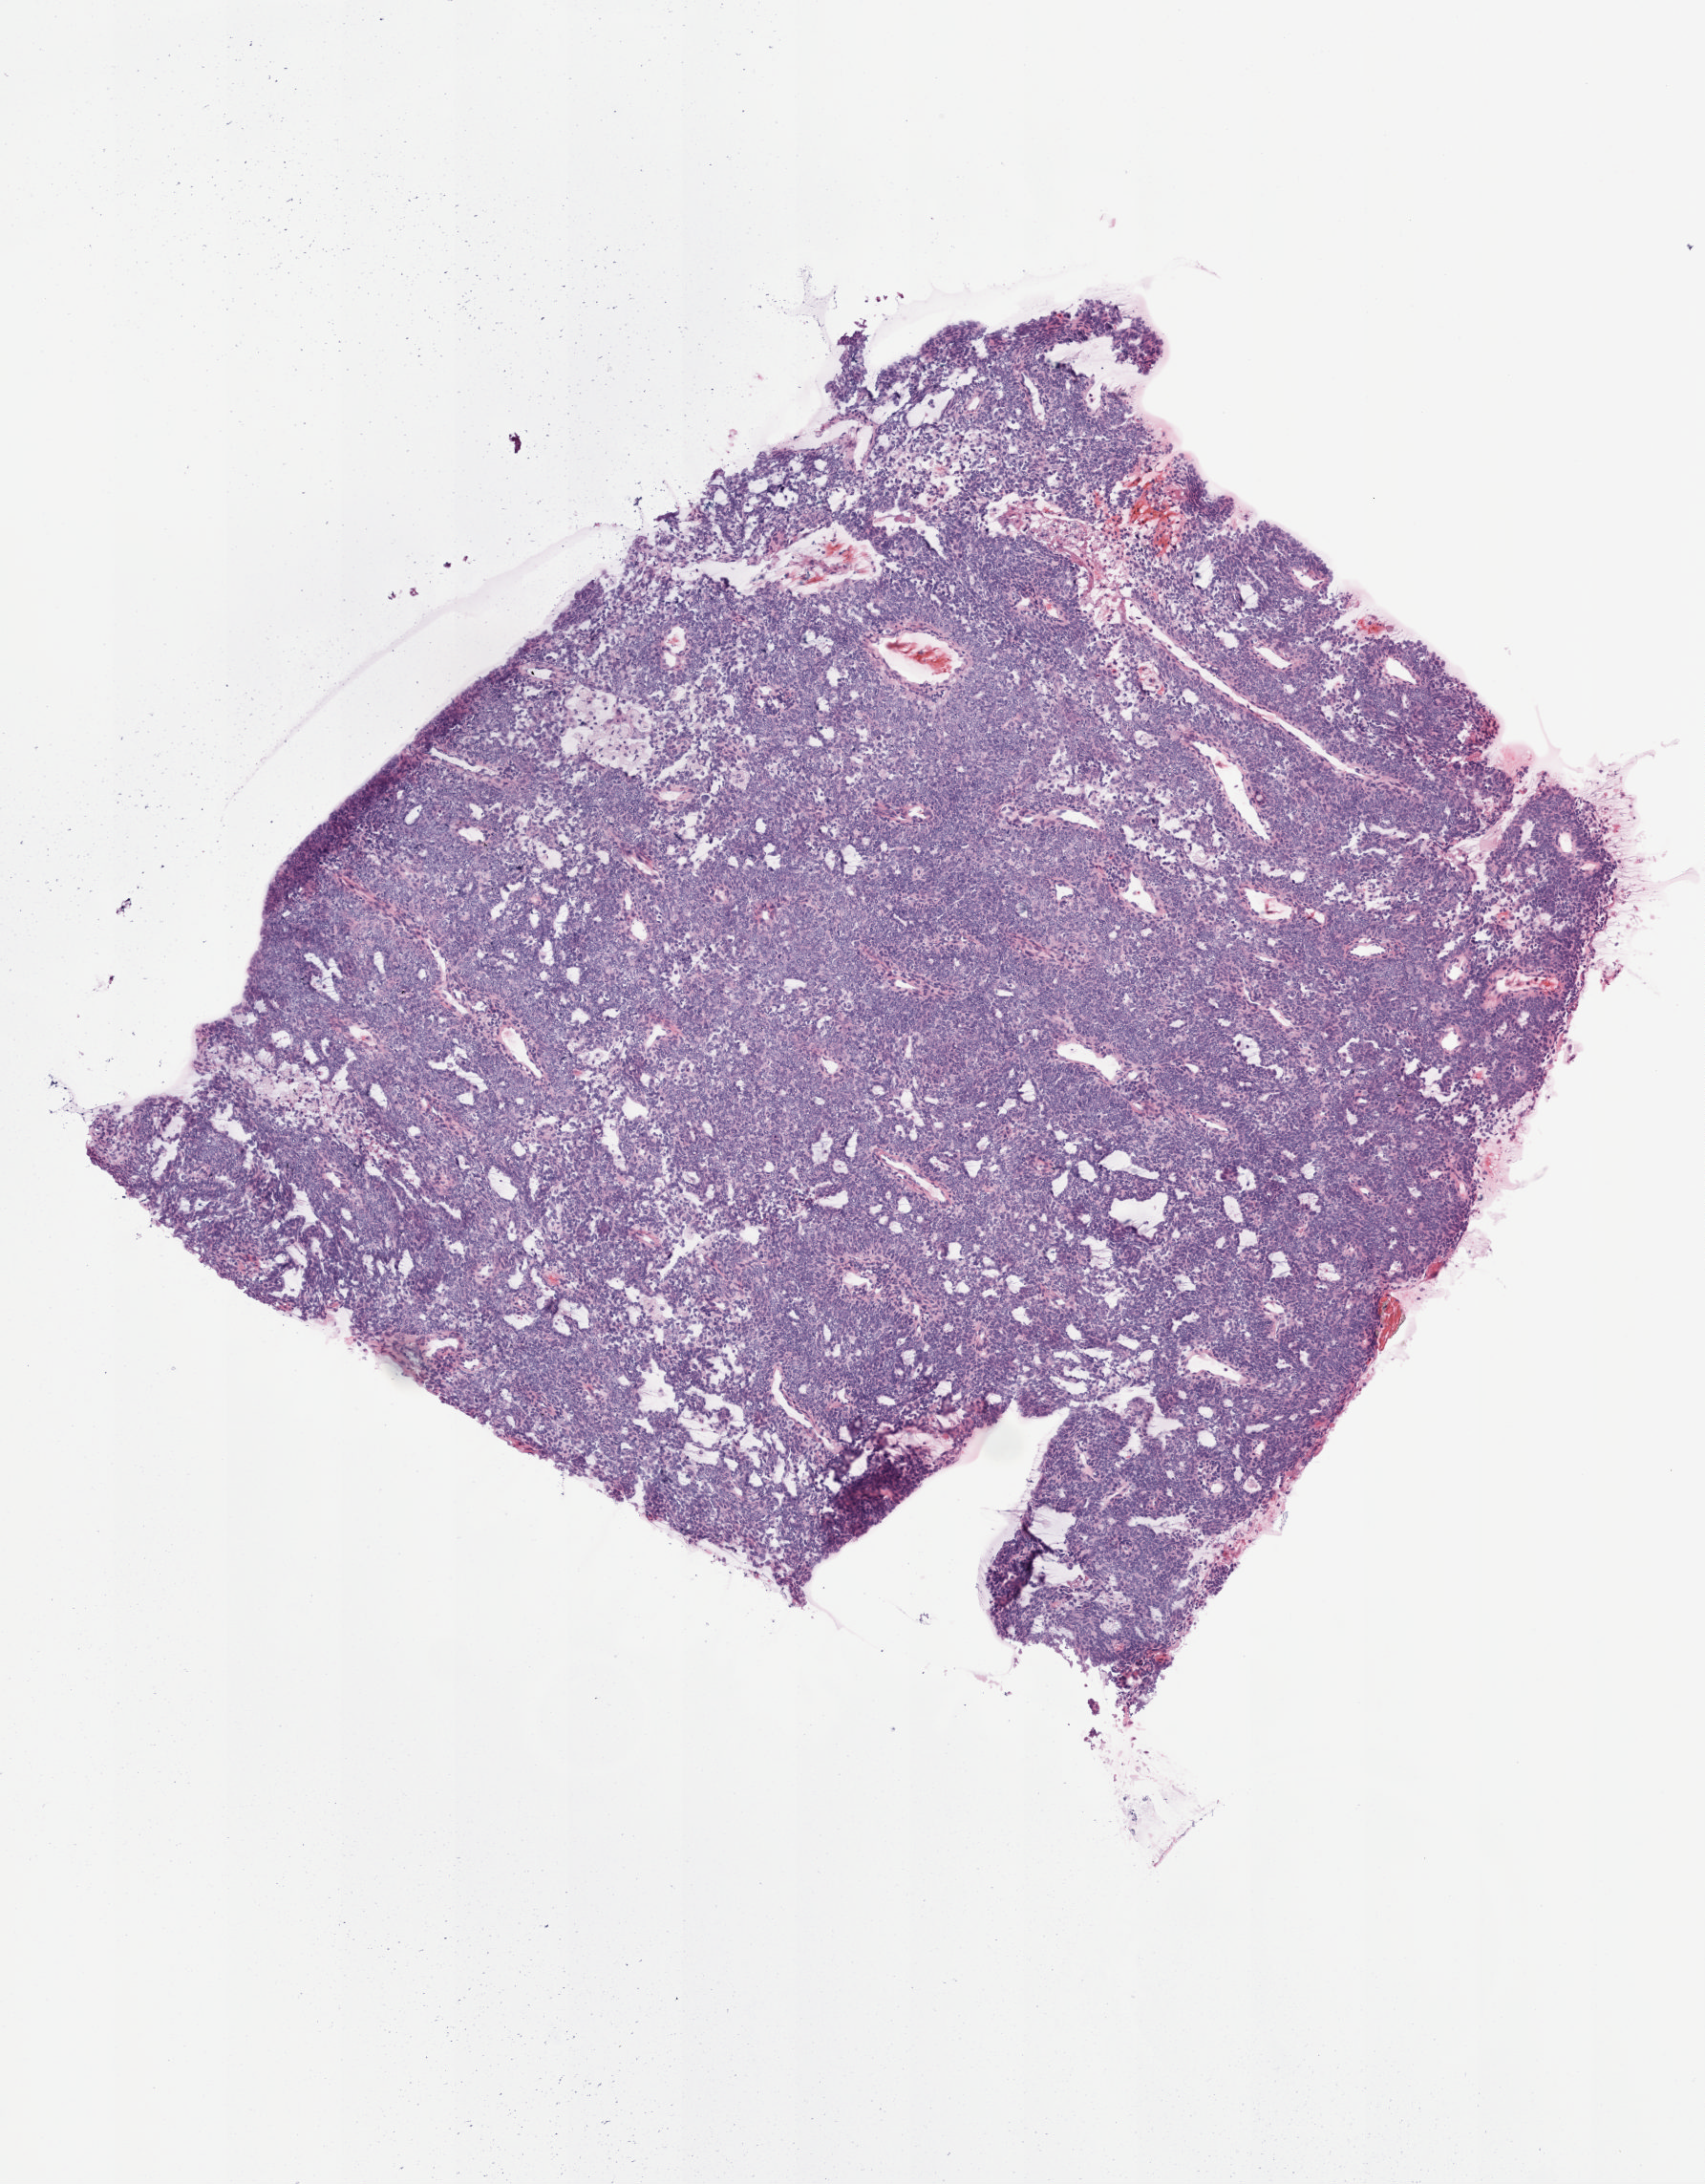
Digitized Hematoxylin and eosin (H&E) stained tissue section (whole slide) — shown as a low-resolution overview of the whole scanned area (about 3.5 x 4.5 mm); frozen section from the top of the tissue portion; sample: primary tumour, cervix. Patient: female, age at initial diagnosis 62 years. Histologic grade: G1 (well differentiated). Composition of this section per pathologist review: tumour cells 90%, tumour nuclei 90%, normal cells 0%, stromal cells 10%, necrosis 0%. Inflammatory infiltration, as recorded: lymphocyte infiltration 40%, monocyte infiltration 10%, neutrophil infiltration 20%.
Histologic diagnosis: Squamous cell carcinoma, NOS (cervix uteri). FIGO stage: IIB. Lymph nodes positive (case pathology): 0 of 26 examined.